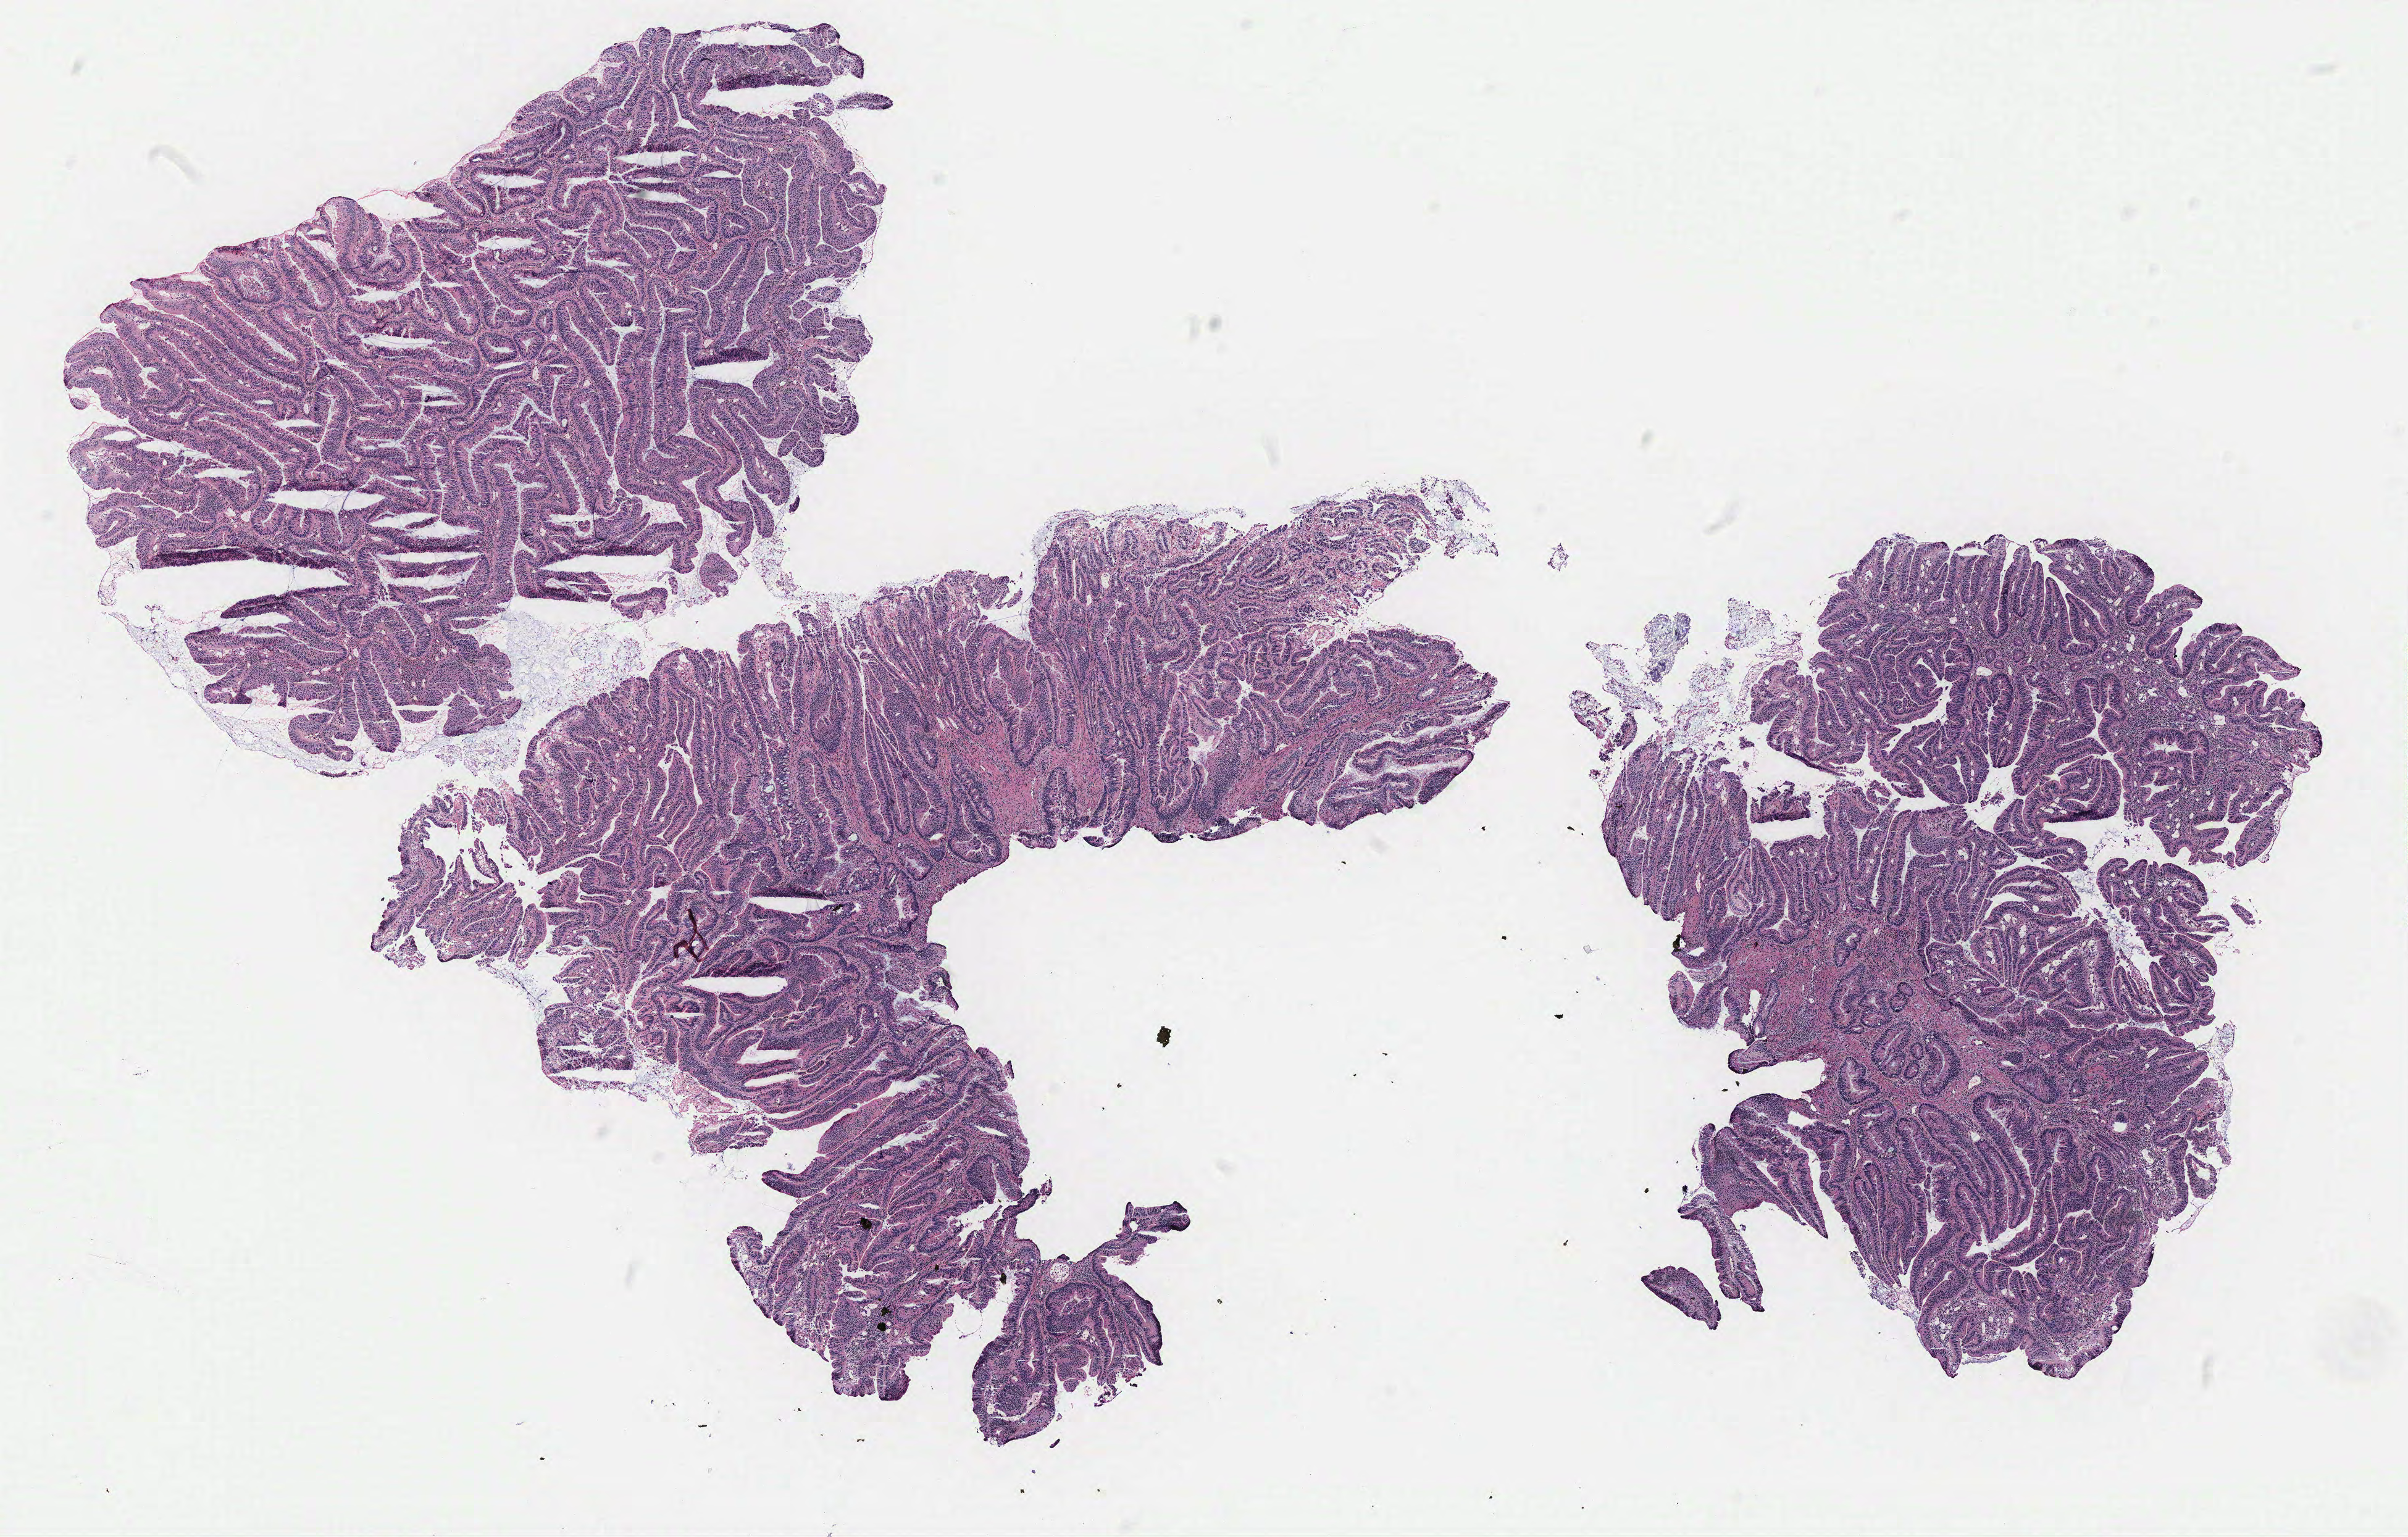
Whole-slide histology image, H&E-stained — shown as a low-resolution overview of the whole scanned area (about 15.6 x 10.0 mm), normal (non-tumour) tissue sample, colon. Patient: female, age 54 years.
This section: normal (non-tumour) tissue from the same patient. Patient diagnosis: Adenocarcinoma, NOS.